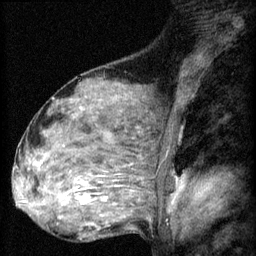
Breast MRI (dynamic contrast-enhanced), one sagittal slice. Position 39 of 60 along the scan axis. 3 images stored at this slice position (order not interpretable as contrast timing). 1.5 T. TE 4.2 ms, TR 8.2 ms. 2 mm slice thickness. 256 × 256 image matrix, field of view 180 × 180 mm. Female patient, age 48 years.
Structures marked on this image (semi-automatically segmented with operator editing):
- analysis volume of interest (the breast-tissue region the enhancement analysis was run in; not a lesion): bounding box [x1, y1, x2, y2] px = [48, 160, 125, 217]
- tumour enhancement mask (voxels above the 70 % enhancement threshold inside the analysis volume of interest): [62, 182, 107, 205]